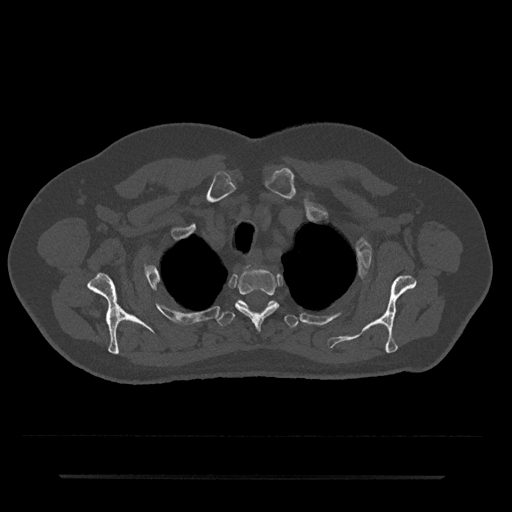
CT including the spine, one axial slice; position 595 of 797 along the scan axis; 120 kVp; bone window (W 1800 / L 400 HU); 512 × 512 image matrix, field of view 437 × 437 mm. Patient: male, 69 years. Case-level facts recorded for this patient, not image findings: primary cancer: prostate.
Structures marked on this image (semi-automatic segmentation, software-assisted and operator-edited):
- T2 vertebra: bounding box <235,268,279,330> (left, top, right, bottom; pixels)
- T3 vertebra: <217,300,298,328>